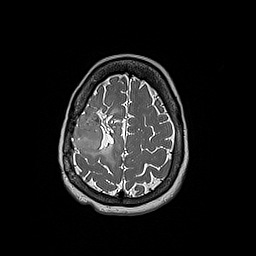
Brain MRI from a brain-tumour surgery series, one axial slice. 1 mm slice thickness. 256 × 256 image matrix. Case-level facts recorded for this patient, not image findings: histopathology: Oligodendroglioma; WHO grade: 3; IDH mutation: yes; tumour location: Right Frontal.
Annotated regions visible in this slice (expert manual segmentation):
- tumour: bounding box <72,112,104,154> (left, top, right, bottom; pixels)